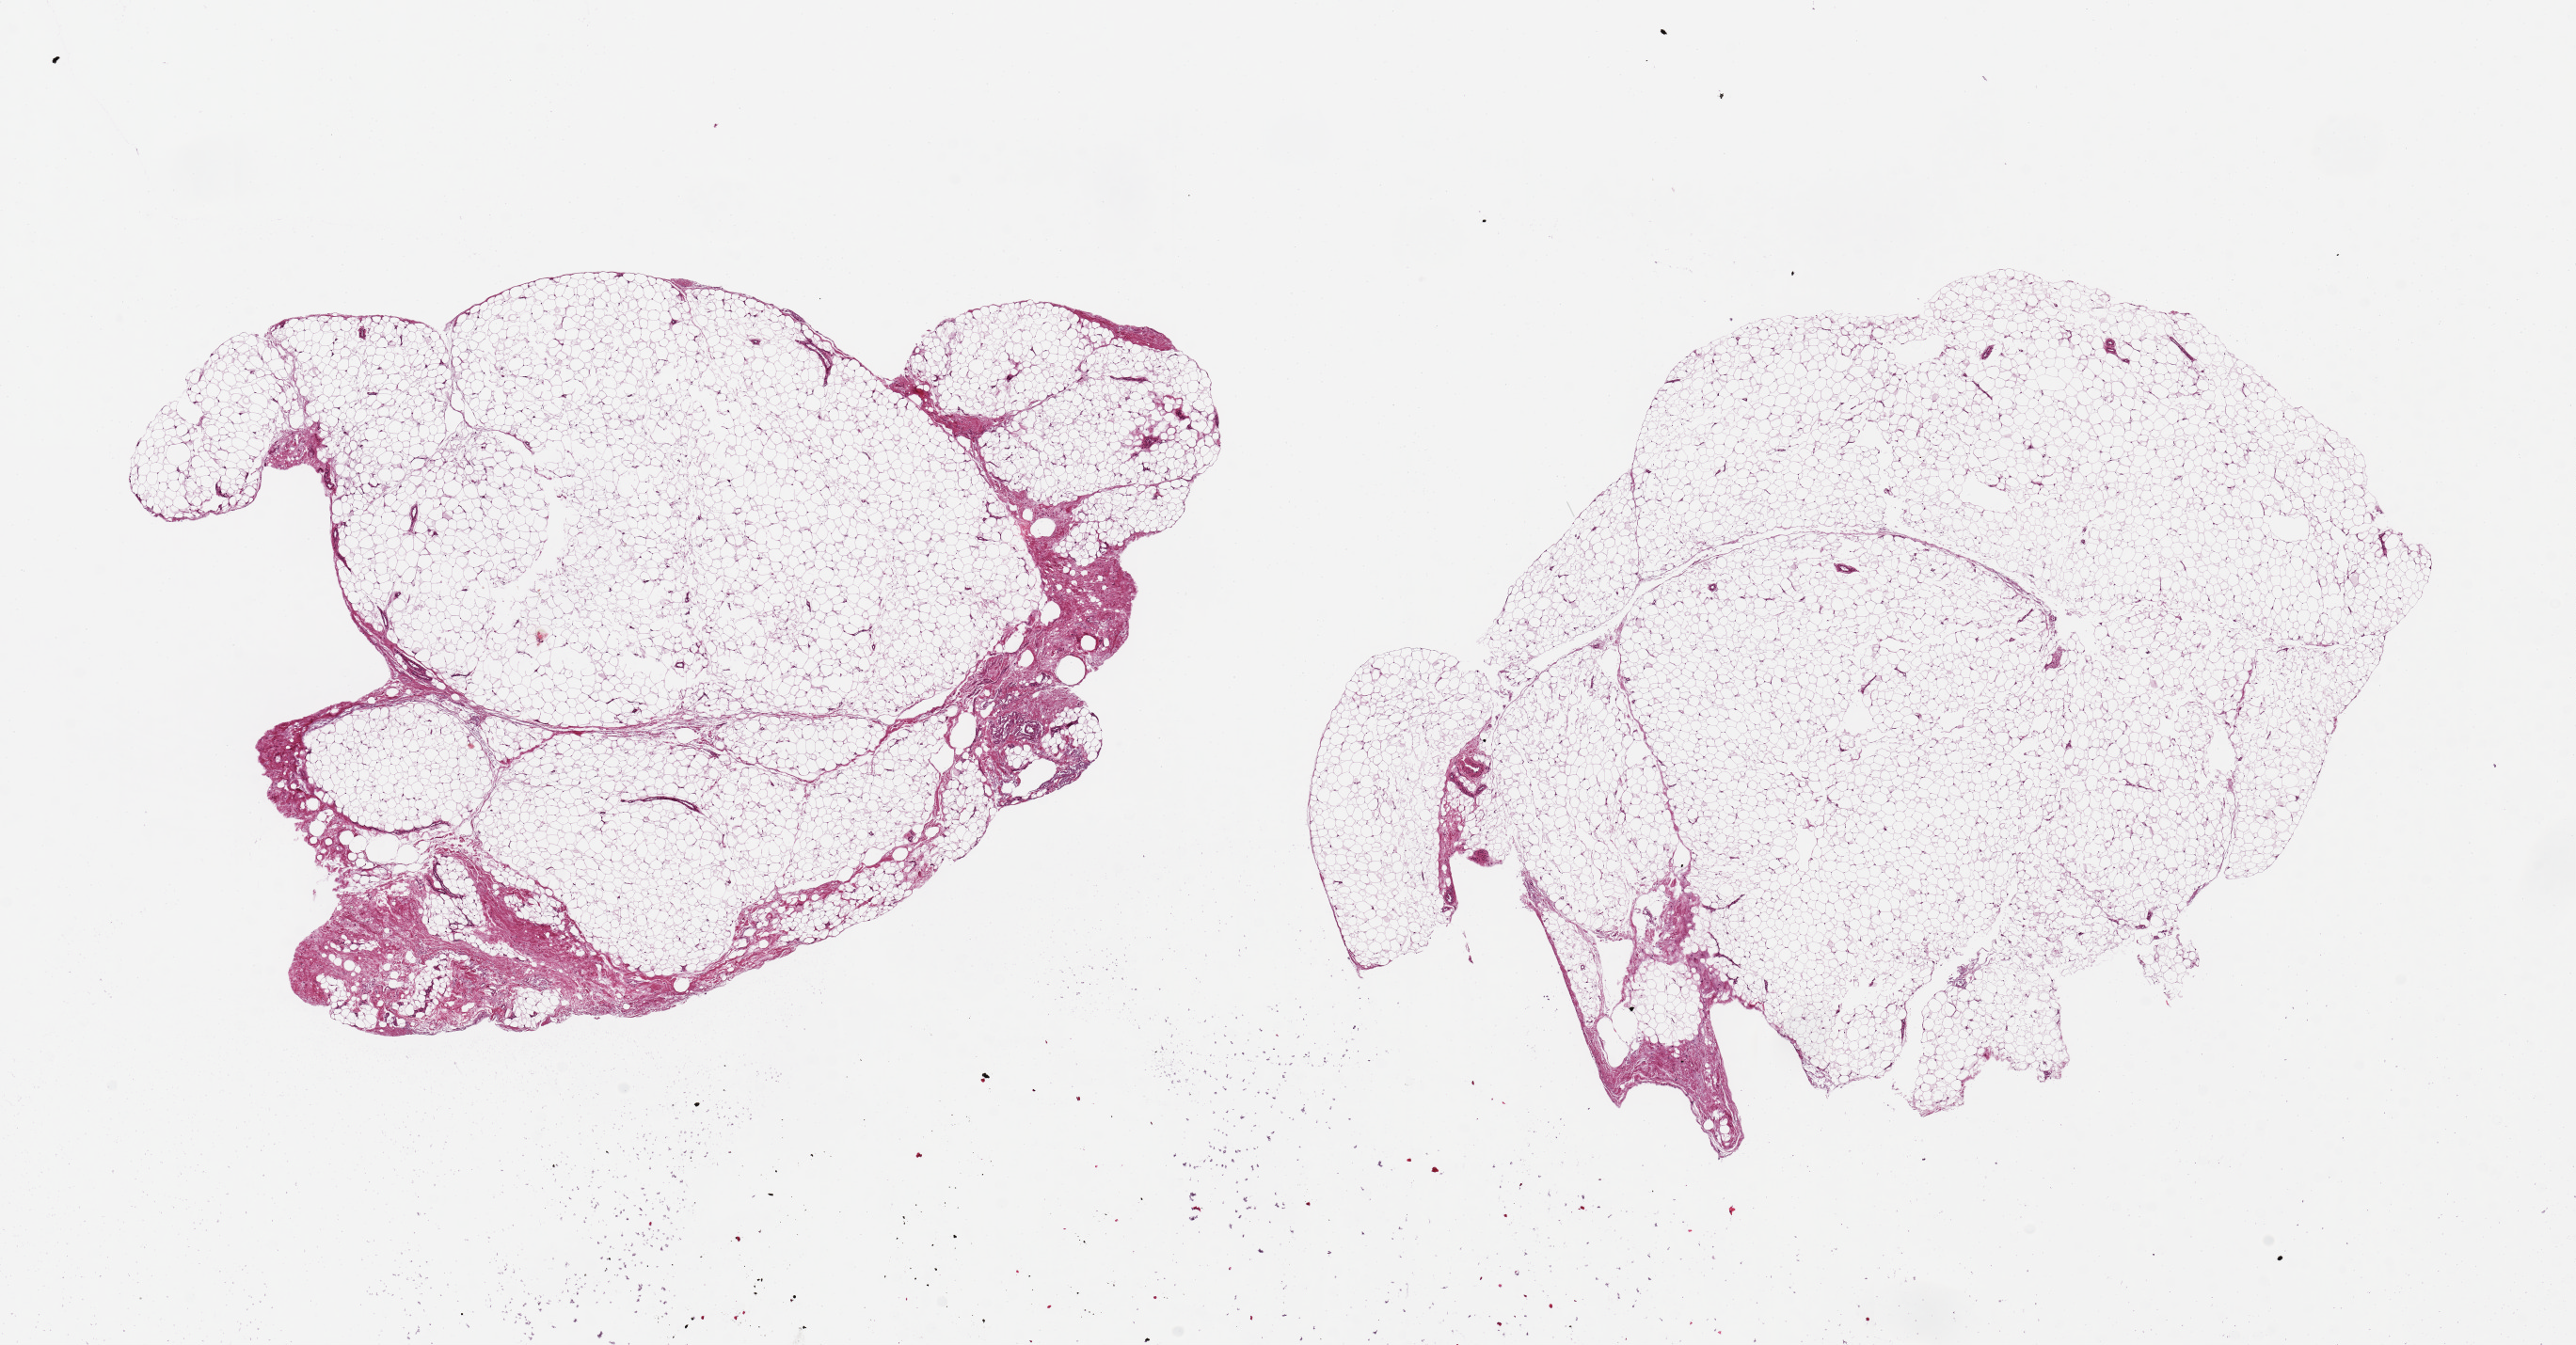
Whole-slide image, H&E stain, a low-resolution overview of the entire scanned area, about 21.7 x 11.3 mm, PAXgene-fixed paraffin-embedded (PFPE) section, section of adipose tissue (target tissue), donor tissue sample. Male donor.
Pathologist's review note for this sample: 2 pieces ~7x6mm.